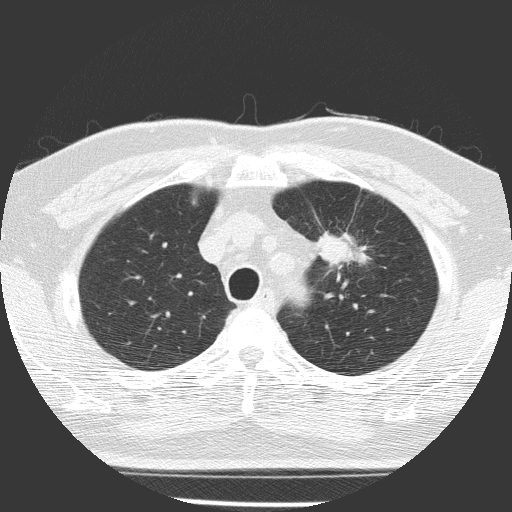
Chest CT (low-dose screening protocol), one axial image. Baseline screening round. Lung window (W 1500 / L -600 HU). Male participant, aged 70 years at enrolment. Current smoker at enrolment.
Lesion marked by an expert reader, bounding box (x1, y1, x2, y2) in pixels: (297, 219, 373, 292). The screening reader recorded 3 non-calcified nodules or masses ≥4 mm on this exam (left upper lobe, left lower lobe, left upper lobe); which of them this box marks is not recorded. Official screen result: positive, change unspecified: nodule(s) >= 4 mm or enlarging nodule(s), mass(es), or other non-specific abnormalities suspicious for lung cancer. Later outcome: lung cancer diagnosed 58 days after this screen — squamous cell carcinoma, NOS, left upper lobe, poorly differentiated (G3), stage IB (AJCC 6th edition), 47 mm at pathology.